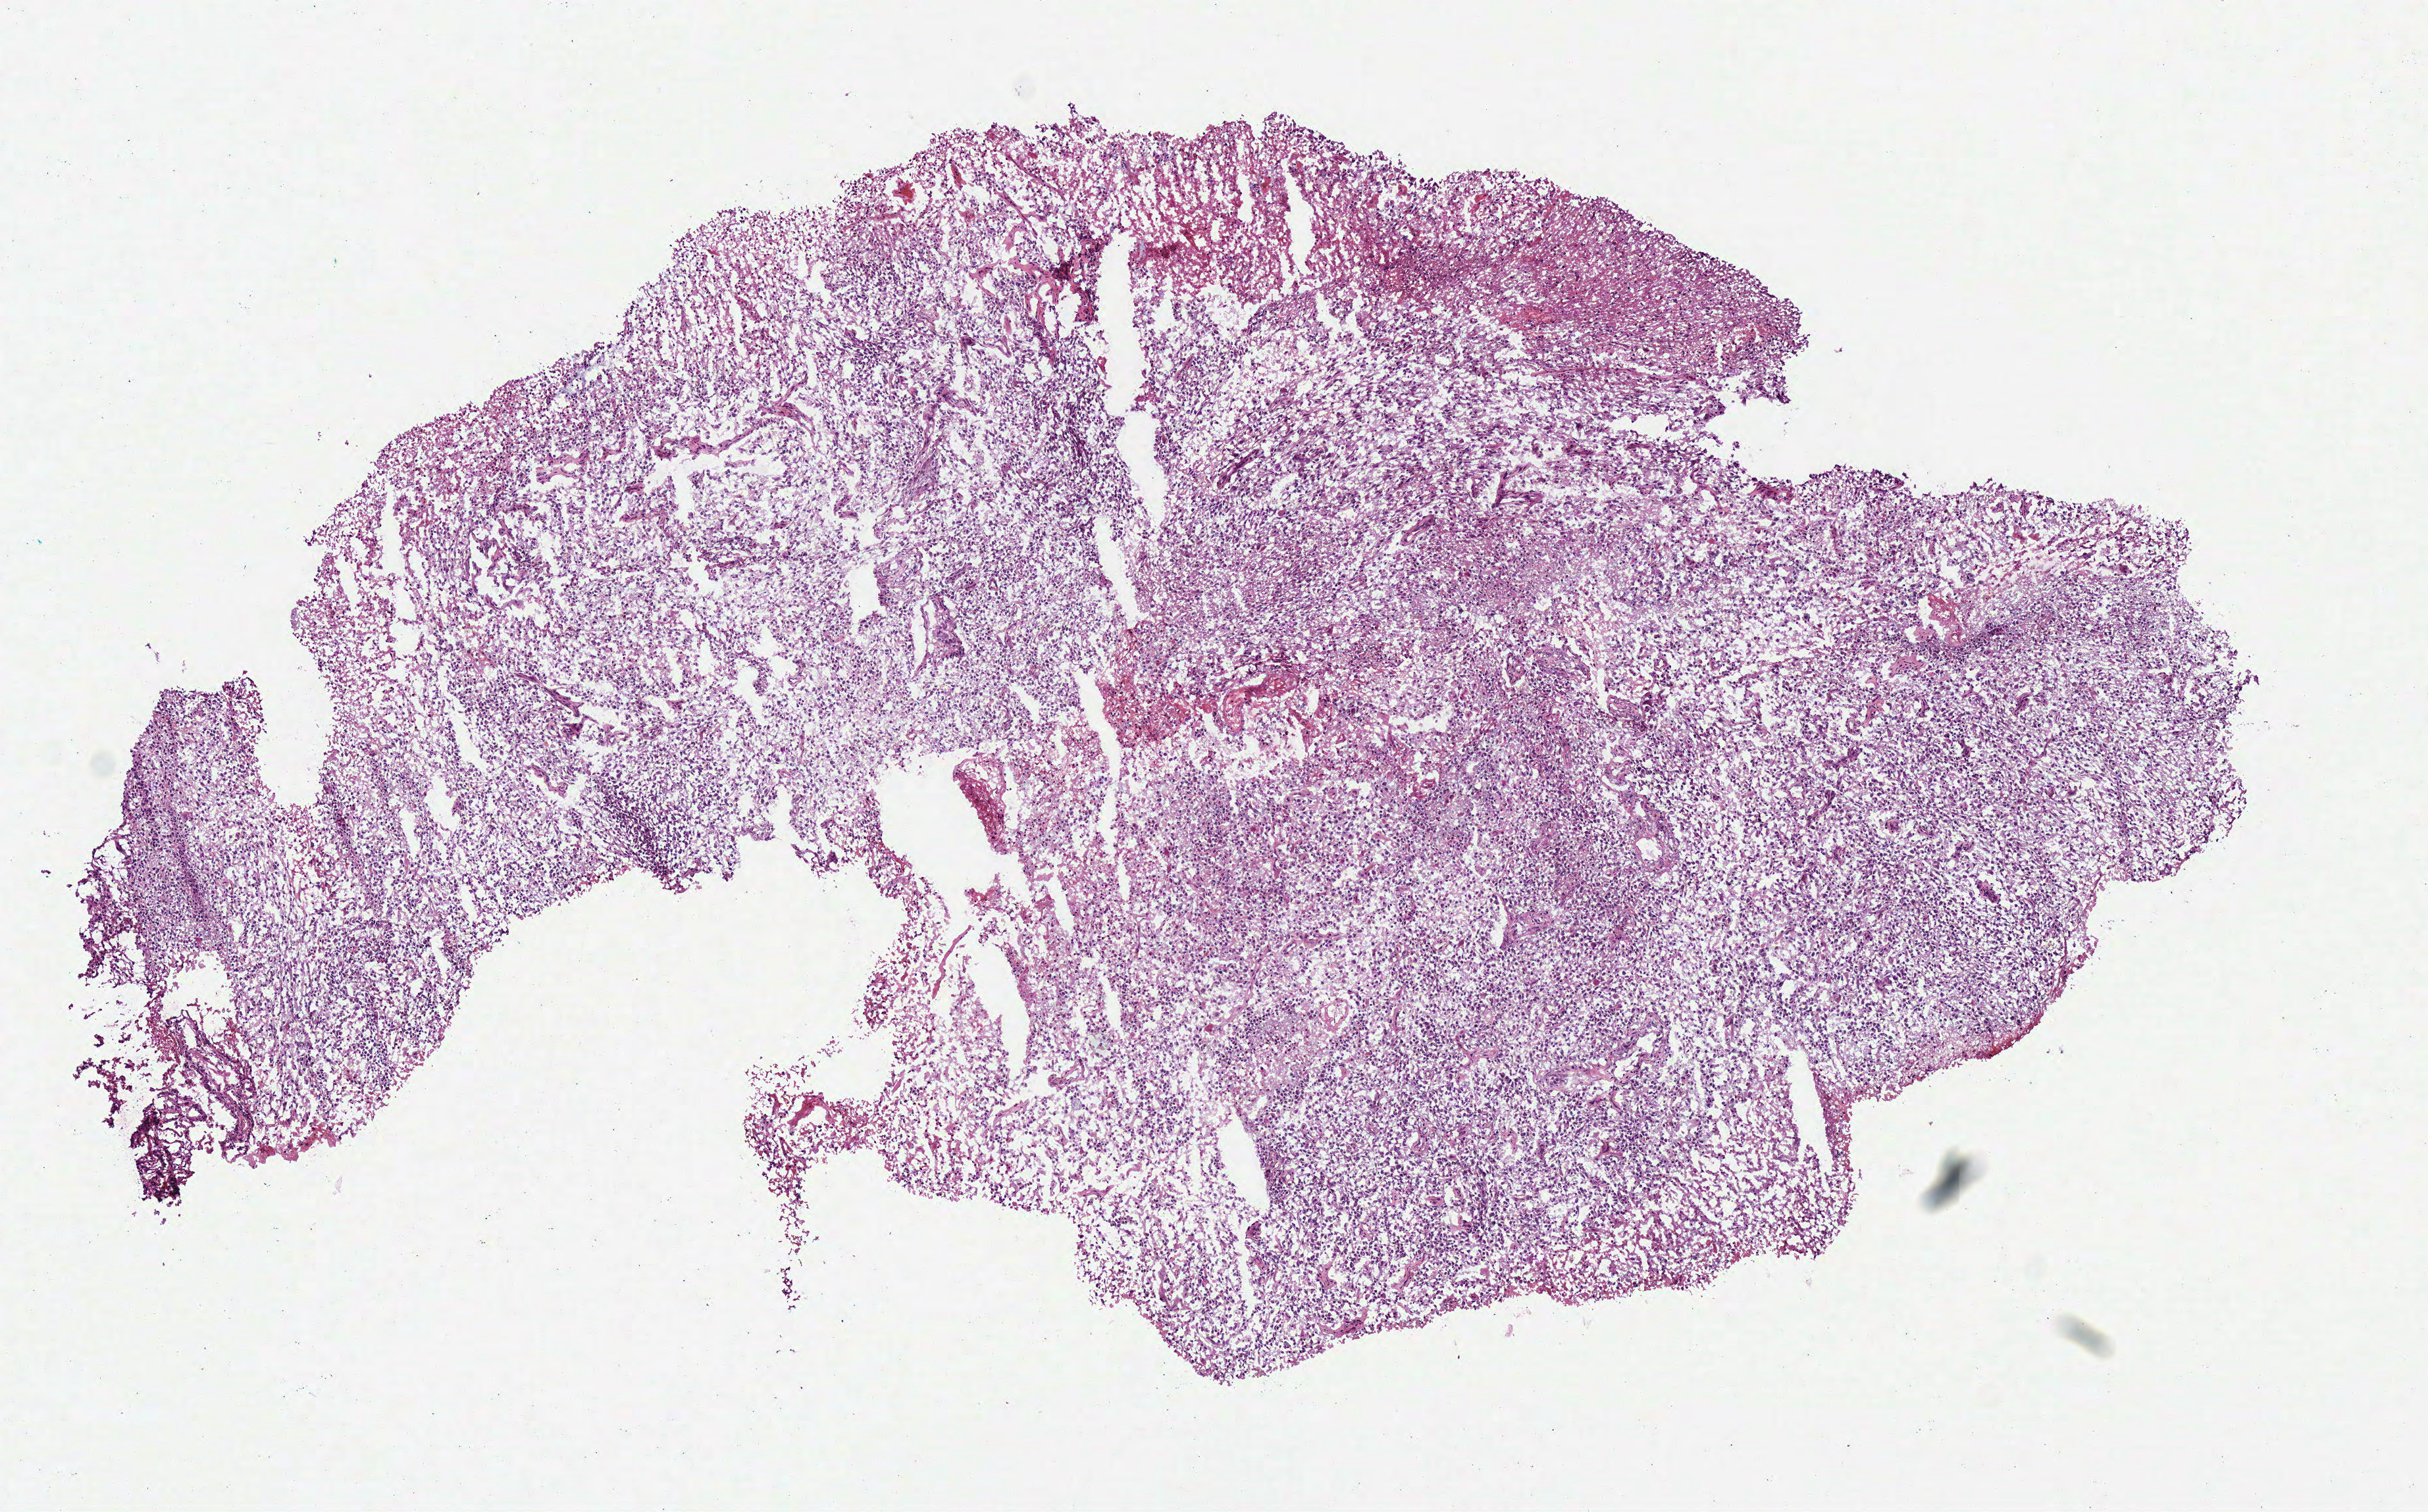
Whole-slide histology image, H&E, low-resolution overview of the scanned area, about 7.3 x 4.5 mm; frozen section from the top of the tissue portion; sample: primary tumour, brain. Male, age 61 years at initial diagnosis. Composition of this section per pathologist review: tumour cells 92%, tumour nuclei 80%, normal cells 0%, stromal cells 0%, necrosis 8%.
Diagnosis: Glioblastoma.